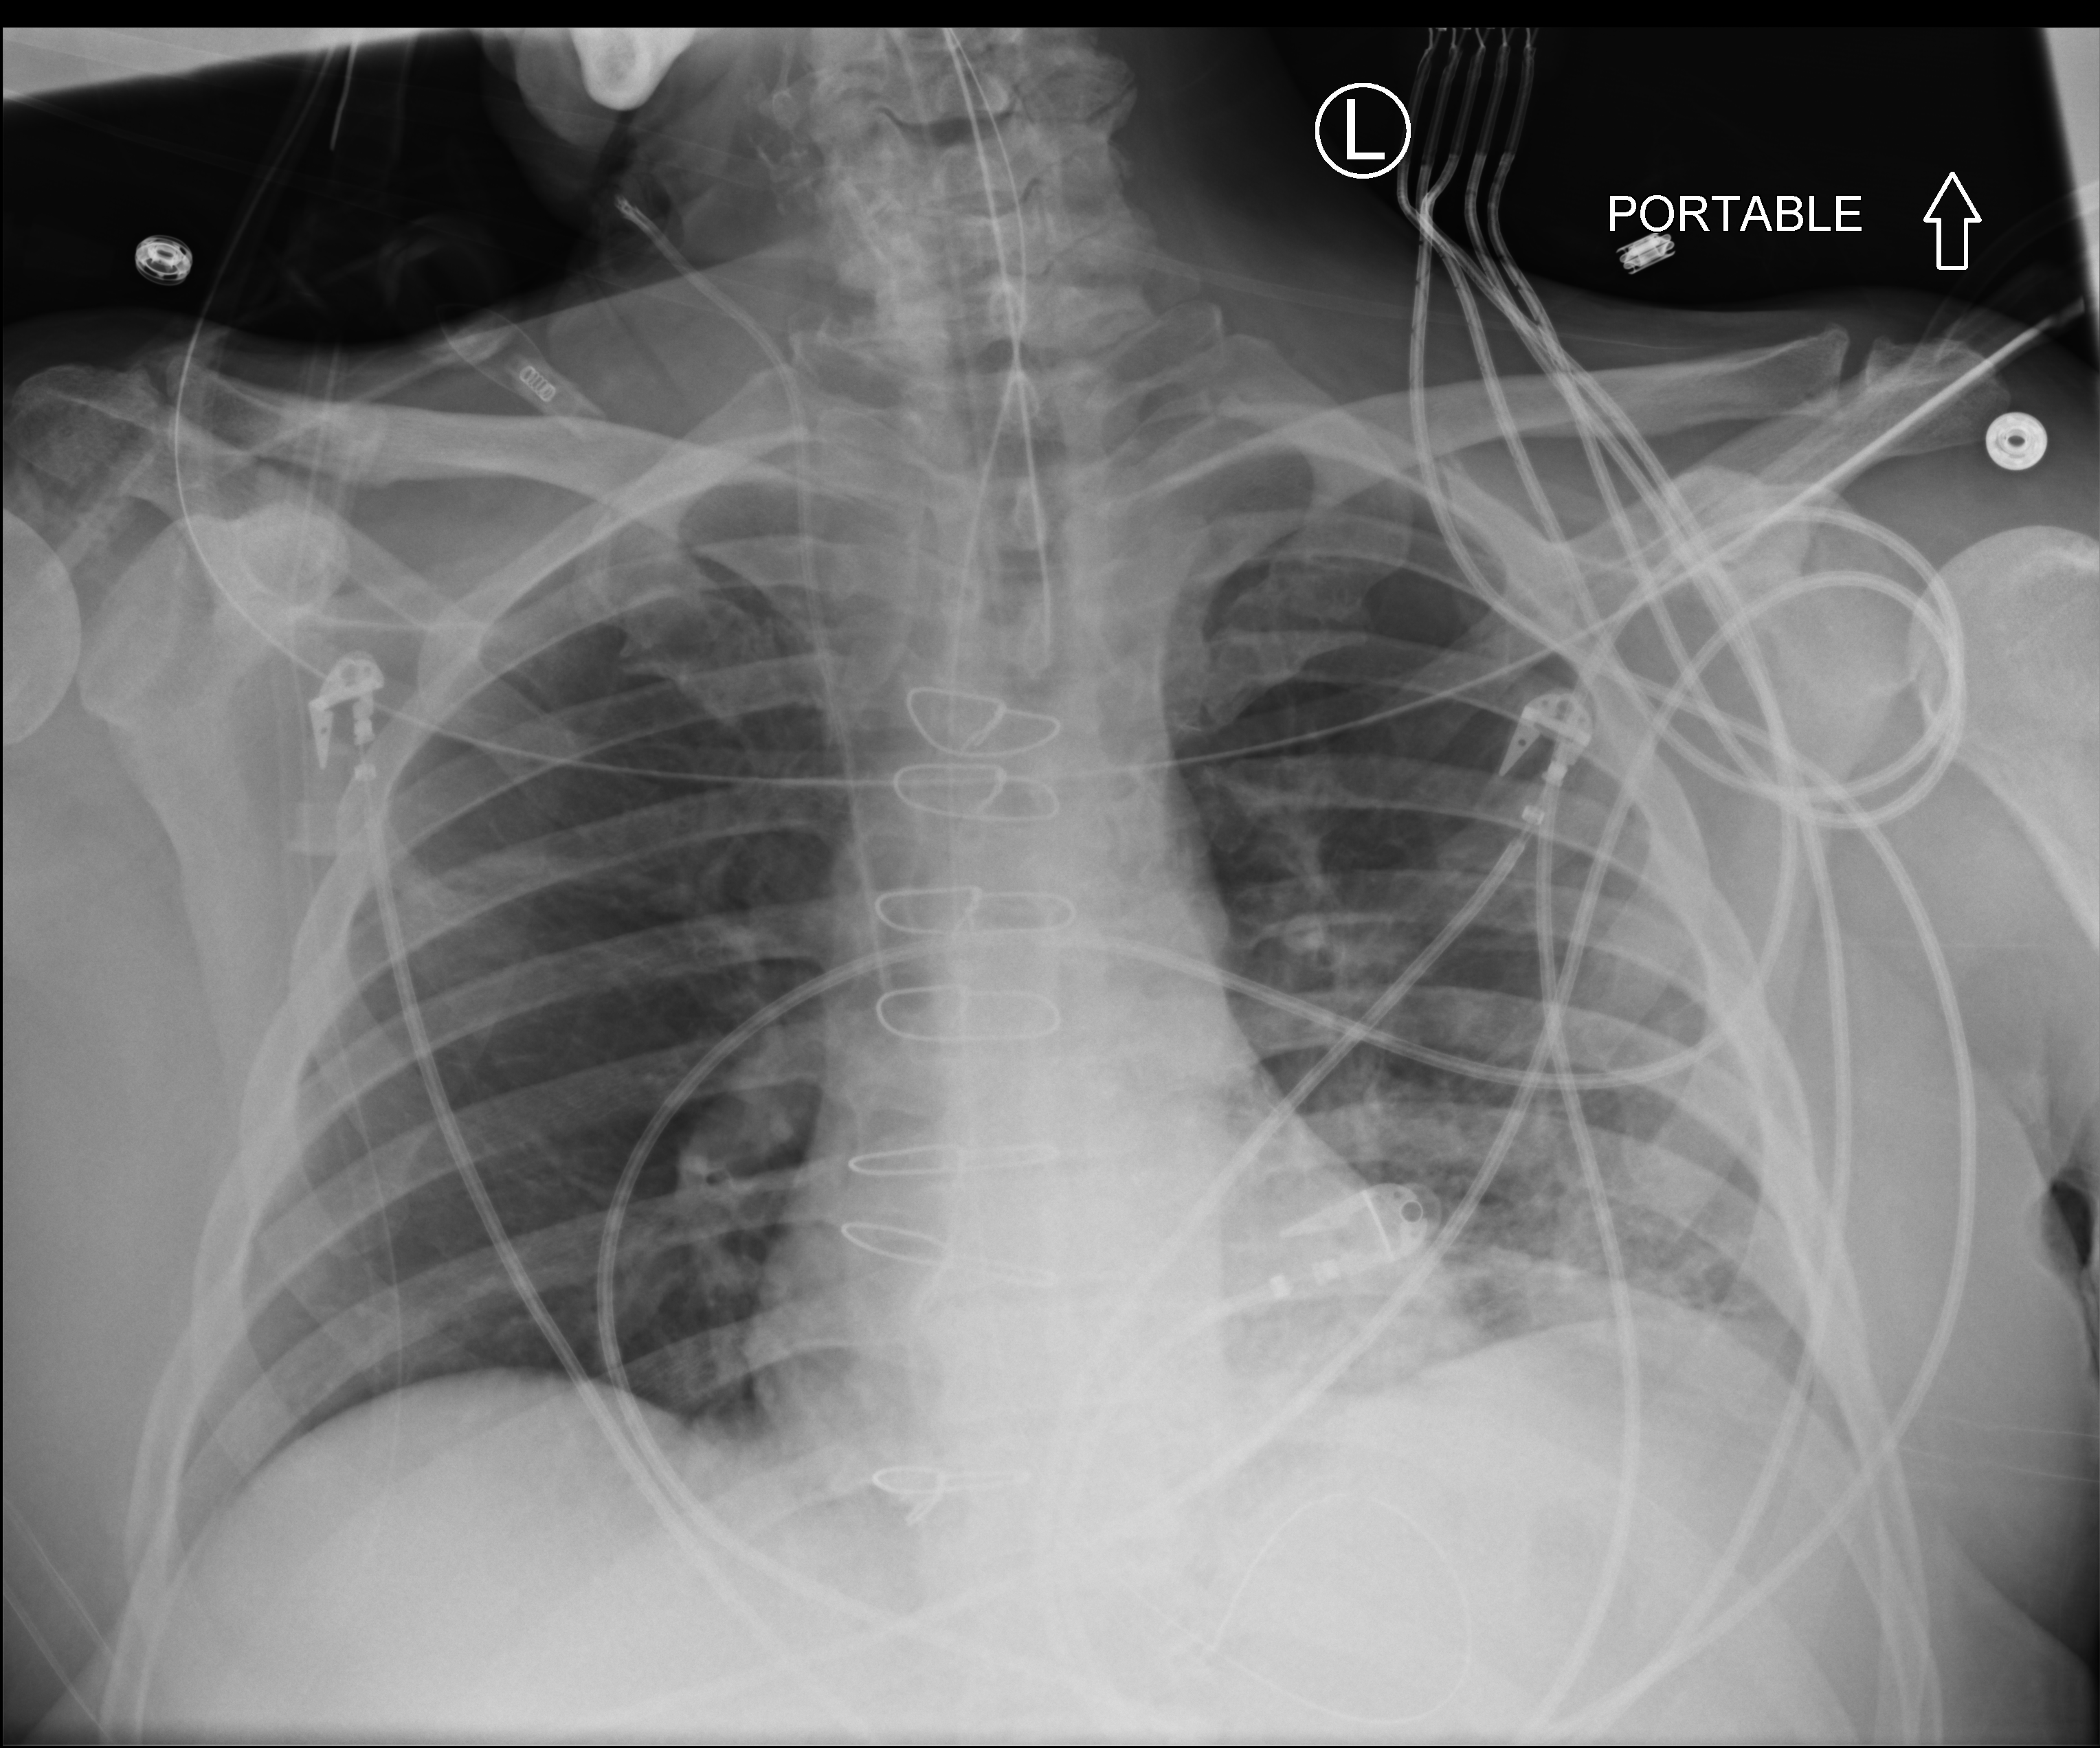
Chest X-ray (portable); anteroposterior (AP) projection. Male patient hospitalised with COVID-19, age 60–74 years.
Hospital-stay facts (about this admission, not read from this image; timing relative to this image not recorded): chronic kidney disease (admission record): no; admitted to intensive care during this hospital stay: yes.